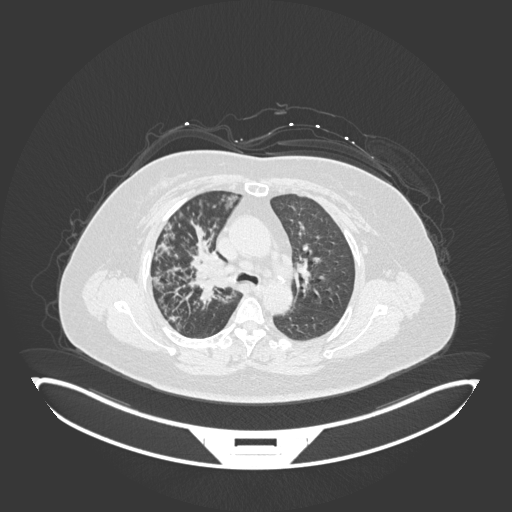
Chest CT, one axial slice. Slice 122 of 245 in the series (ordered by position). Reconstruction kernel B30f. Lung window (W 1500 / L -600 HU). 1 mm slice thickness. 512 × 512 image matrix, field of view 500 × 500 mm. Patient: female, 60 years. Case-level facts recorded for this patient, not image findings: clinical TNM (as recorded): T1c N0 M0; histopathological grade: G1-G2.
Annotated regions visible in this slice (rectangle marked by the reading radiologist):
- lung tumour (recorded histology: squamous cell carcinoma): bounding box <191,255,242,286> (left, top, right, bottom; pixels)